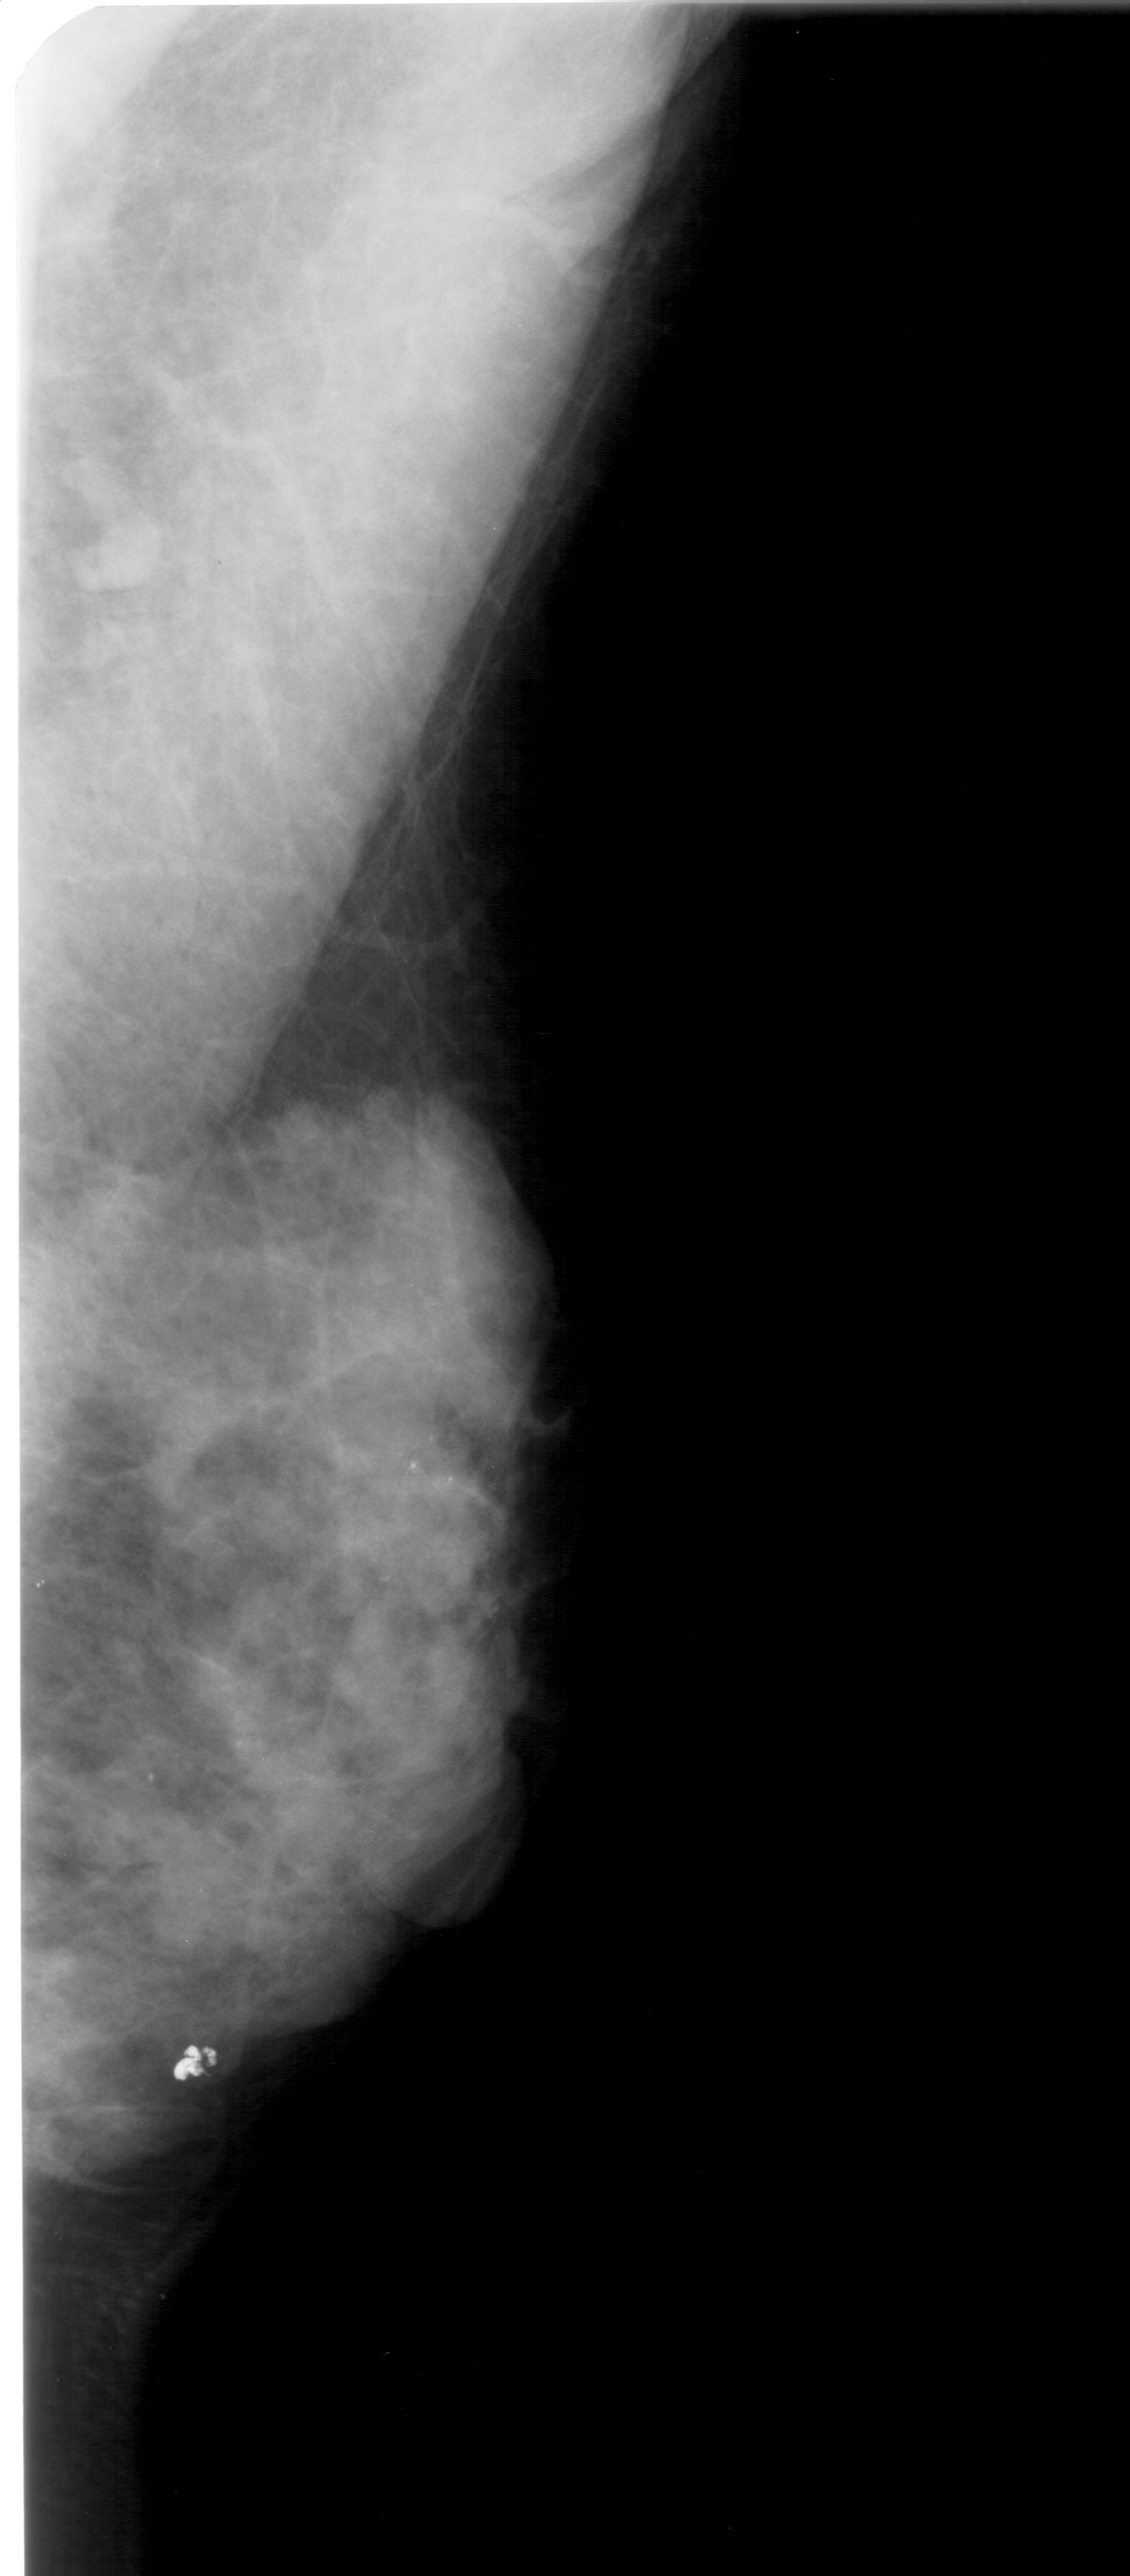
Scanned film-screen mammogram; right breast; MLO view; BI-RADS breast density category 4 (scale 1–4); 1130 × 2576 image matrix.
Expert-marked regions of interest on this film, with their recorded descriptors:
- calcifications, morphology pleomorphic, distribution clustered; BI-RADS assessment category 4; subtlety rating 3 on a 1 (subtle) to 5 (obvious) scale; pathology result (as recorded, not read from the image): malignant: box from (x=361, y=1416) to (x=511, y=1525) px